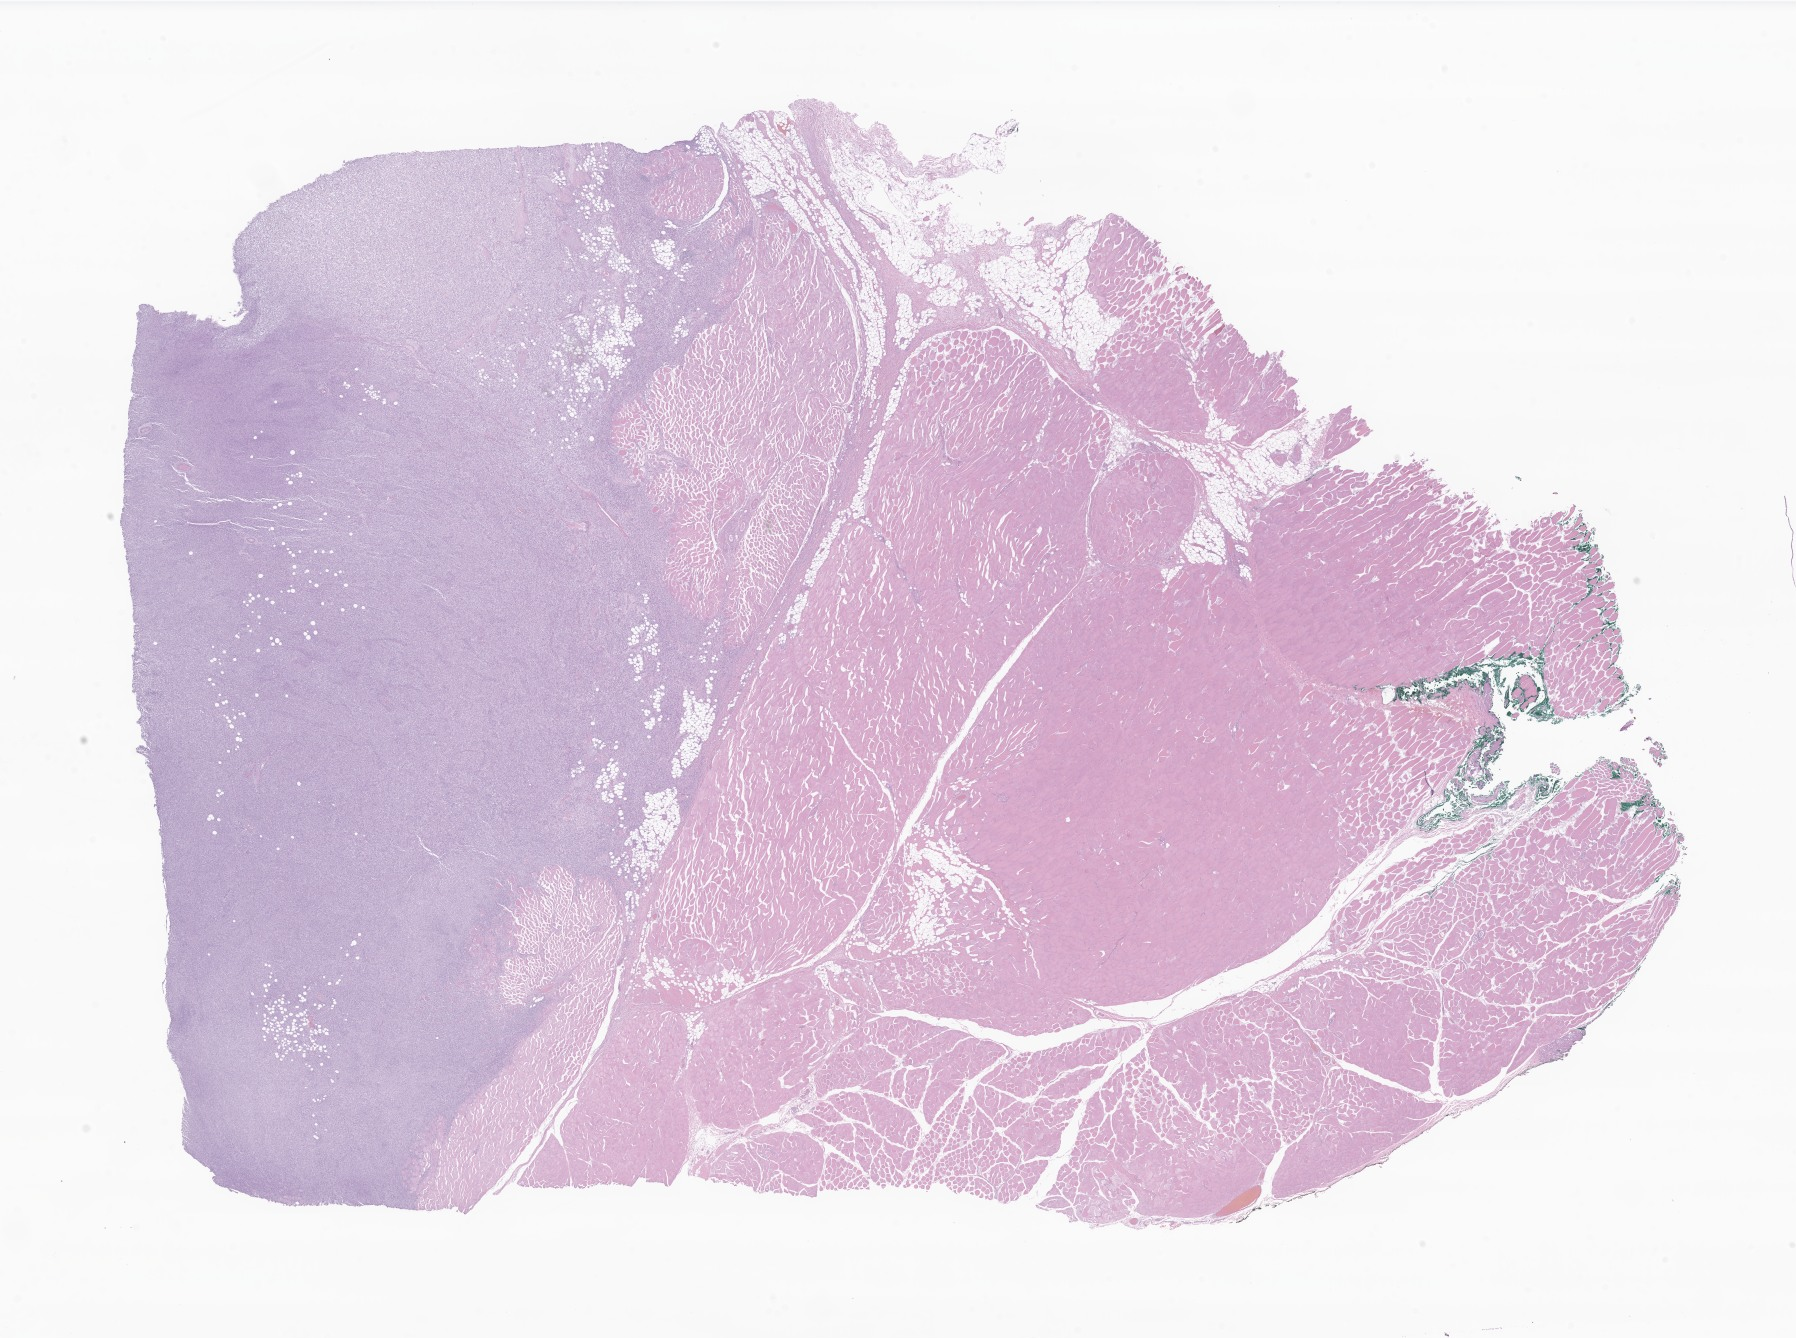
Whole-slide image, H&E stain of tumor tissue, shown as a low-resolution overview of the whole scanned area (about 30.3 x 22.6 mm), formalin-fixed, paraffin-embedded (FFPE) tissue. Patient male; age 241 months.
* recorded diagnosis: Fibrosarcoma, NOS